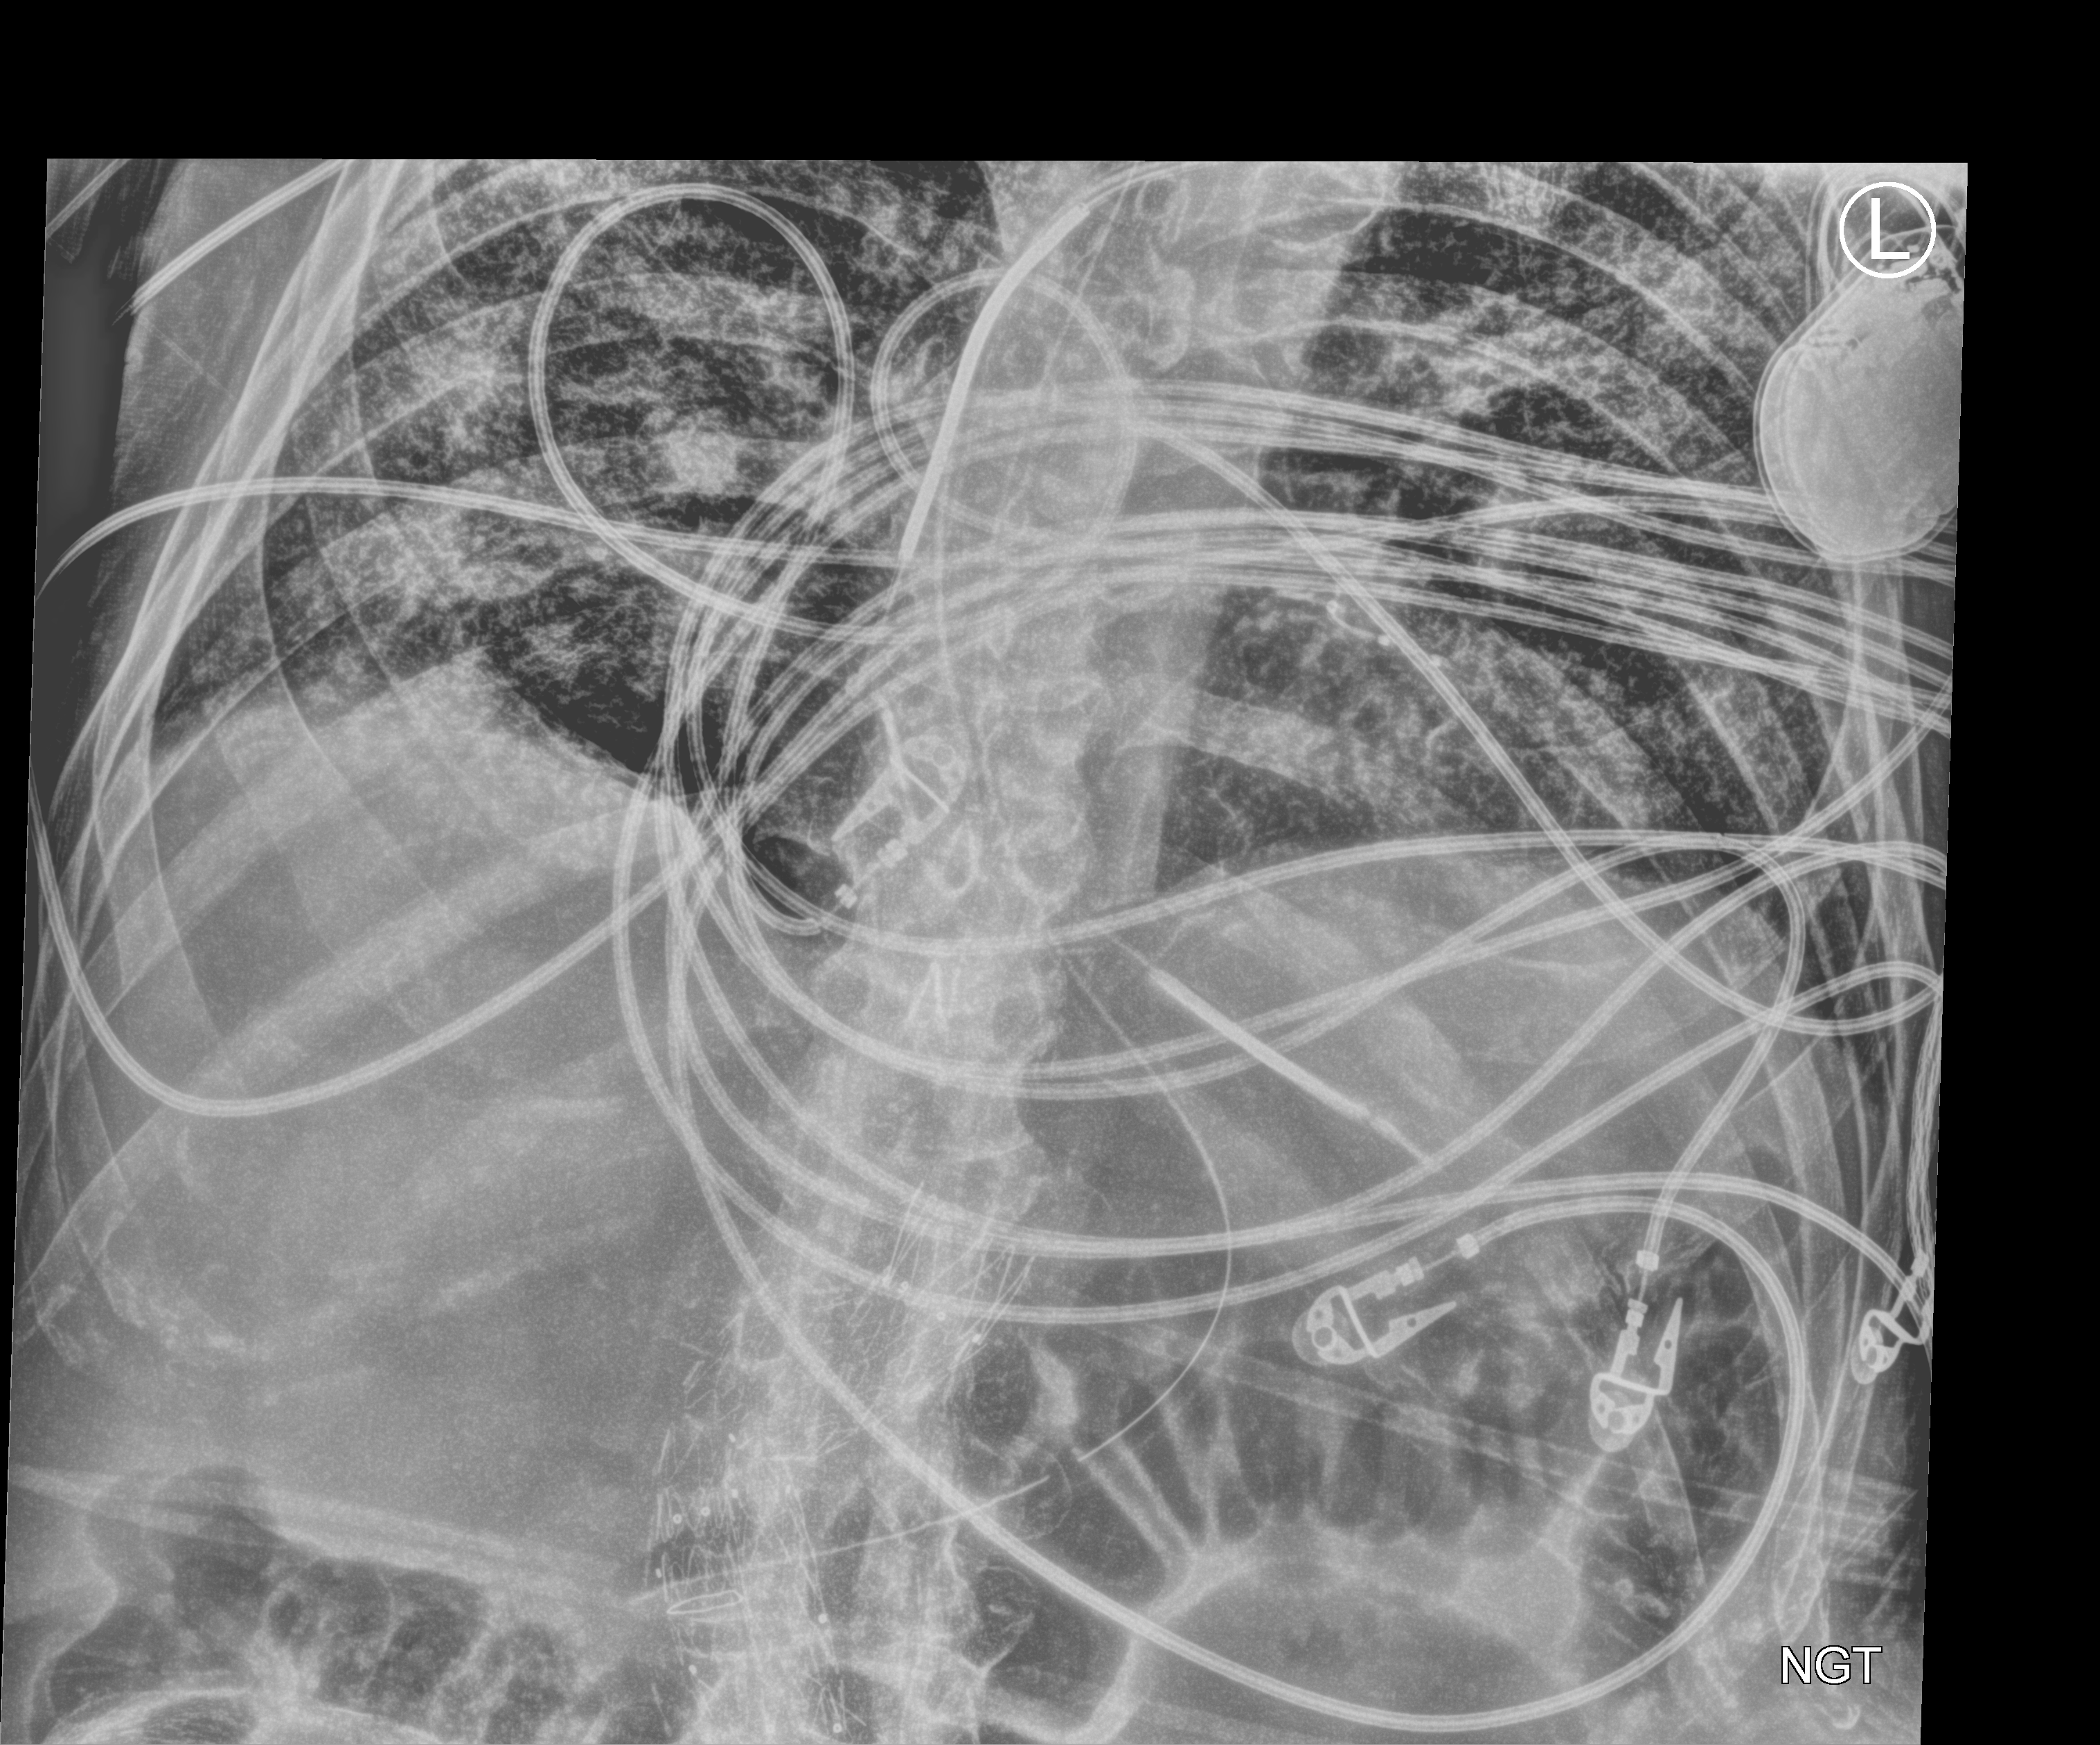
Portable abdomen radiograph, anteroposterior (AP) projection. Patient hospitalised with COVID-19; male, aged 60–74 years.
Hospital-stay facts (about this admission, not read from this image; timing relative to this image not recorded): admitted to intensive care during this hospital stay: yes.